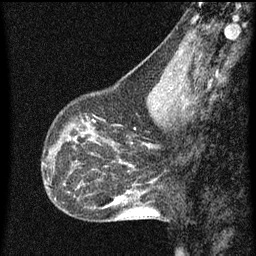
Breast MRI (dynamic contrast-enhanced), one sagittal slice; slice 23 of 60 in the series (ordered by position); dynamic contrast-enhanced series, image 2 of 3 at this slice position (ordered by acquisition); 1.5 T; TE 4.2 ms, TR 8 ms; 2 mm slice thickness; 256 × 256 image matrix, field of view 180 × 180 mm. Patient: female, 43 years.
Annotated regions visible in this slice (semi-automatic segmentation, software-assisted and operator-edited):
- analysis volume of interest (the breast-tissue region the enhancement analysis was run in; not a lesion): bounding box [x1, y1, x2, y2] px = [53, 104, 101, 151]
- tumour enhancement mask (voxels above the 70 % enhancement threshold inside the analysis volume of interest): [69, 120, 94, 143]